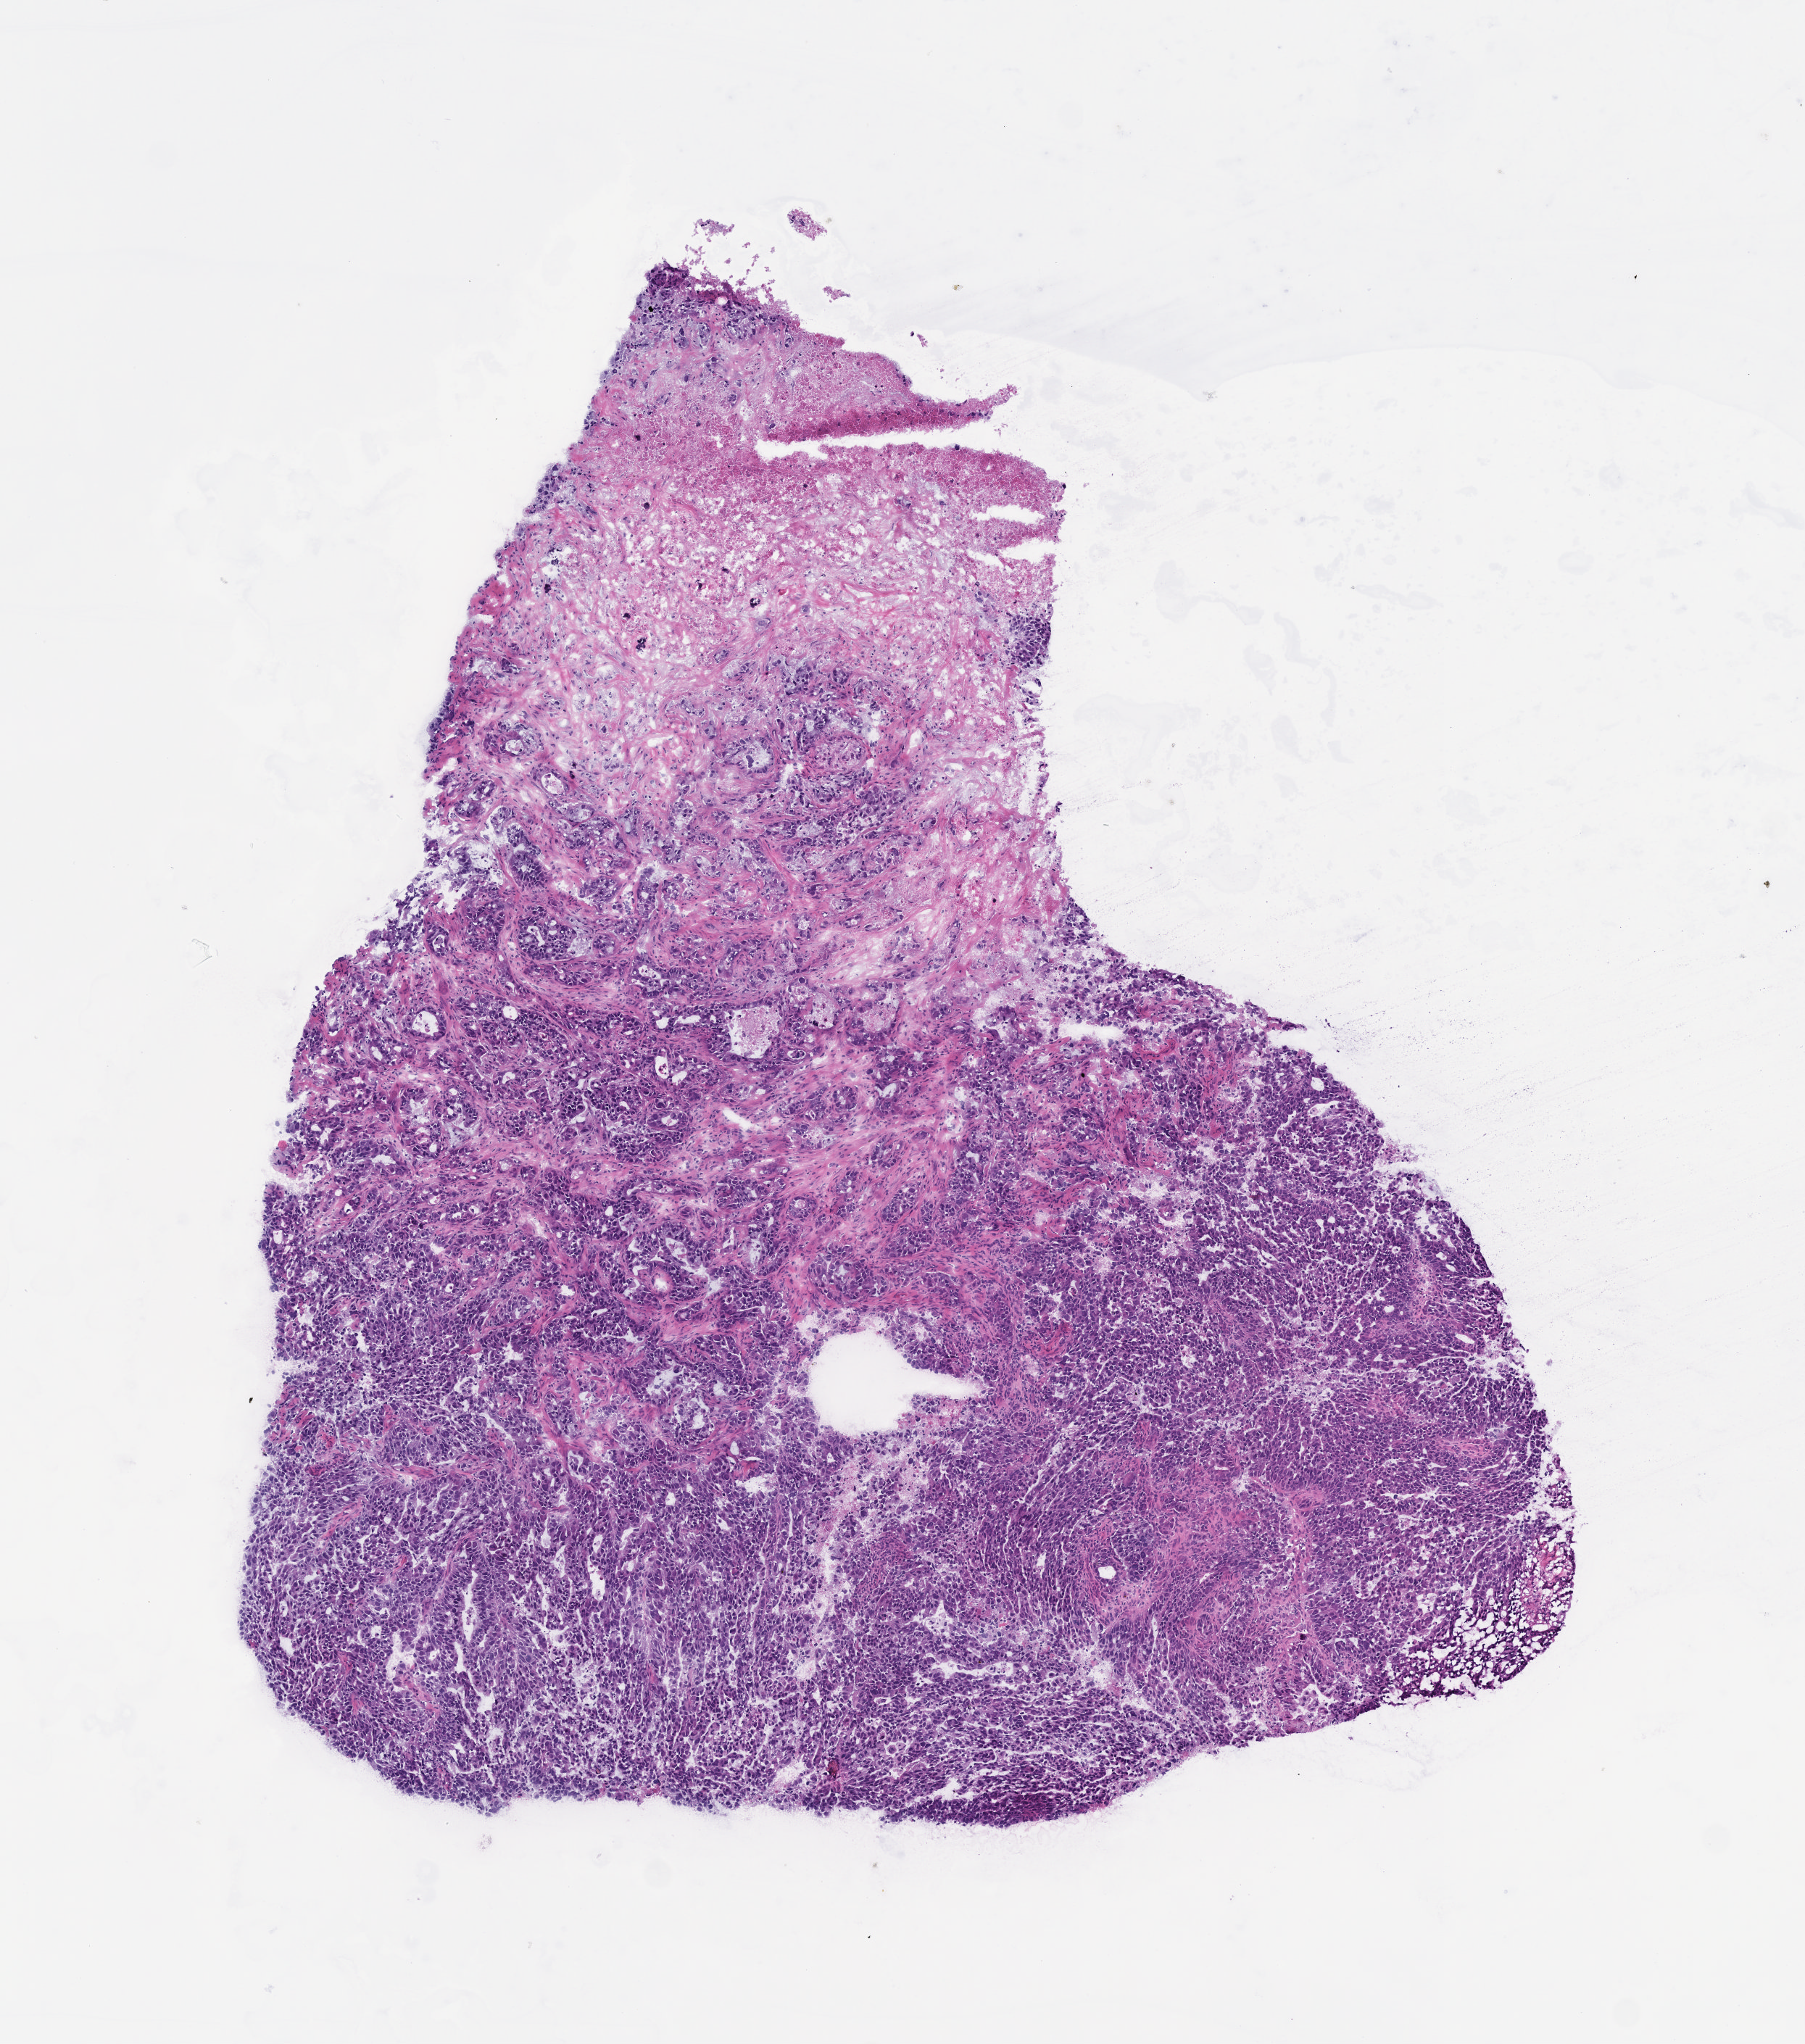
H&E whole-slide image of a patient-derived xenograft (PDX) tumor grown in a mouse, passage 1 — a low-resolution overview of the entire scanned area, about 5.0 x 5.7 mm; formalin-fixed paraffin-embedded section; tumor site category: pancreas.
Originating patient diagnosis: Pancreatic Adenocarcinoma.